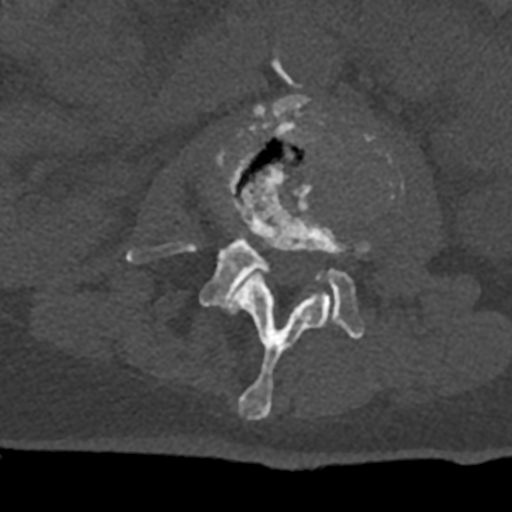
CT including the spine, one axial slice; slice 350 of 797 in the series (ordered by position); reconstruction kernel Br40s/3; 120 kVp; bone window (W 1800 / L 400 HU); 0.5 mm slice thickness; 512 × 512 image matrix. Patient: male, 74 years. Case-level facts recorded for this patient, not image findings: primary cancer: renal.
Structures marked on this image (semi-automatically segmented with operator editing):
- L2 vertebra: bounding box [x1, y1, x2, y2] px = [219, 114, 371, 420]
- L3 vertebra: [126, 94, 400, 339]